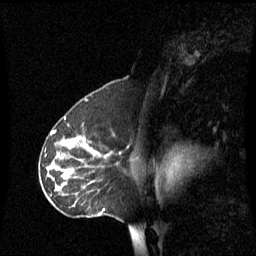
Breast MRI (dynamic contrast-enhanced), one sagittal slice; slice 40 of 60 in the series (ordered by position); dynamic contrast-enhanced series, image 2 of 3 at this slice position (ordered by acquisition); 1.5 T; TE 4.2 ms, TR 8.4 ms; 256 × 256 image matrix, field of view 240 × 240 mm. Patient: female, 45 years. Case-level facts recorded for this patient, not image findings: setting: breast cancer imaged before/during neoadjuvant chemotherapy; receptor status: HR-positive, HER2-negative.
Outlined on this slice (semi-automatic segmentation, software-assisted and operator-edited):
- analysis volume of interest (the breast-tissue region the enhancement analysis was run in; not a lesion): box from (x=40, y=124) to (x=117, y=217) px
- tumour enhancement mask (voxels above the 70 % enhancement threshold inside the analysis volume of interest): (x=64, y=154)–(x=99, y=175)